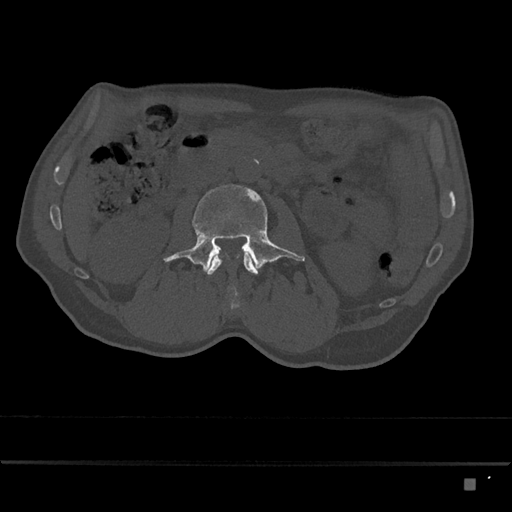
CT including the spine, one axial slice; slice 427 of 797 in the series (ordered by position); 120 kVp; bone window (W 1800 / L 400 HU); 0.5 mm slice thickness; 512 × 512 image matrix, field of view 390 × 390 mm. Patient: male, 72 years. From the clinical record (not read from this slice): primary cancer: prostate.
Annotated regions visible in this slice (semi-automatically segmented with operator editing):
- L2 vertebra: bounding box <203,253,258,275> (left, top, right, bottom; pixels)
- L3 vertebra: <164,184,305,294>